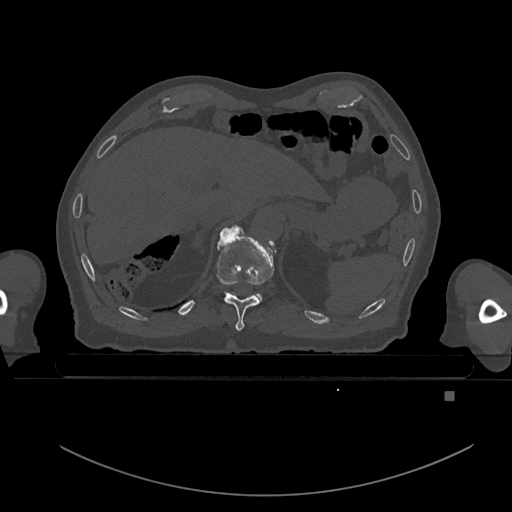
CT including the spine, one axial slice. Slice 76 of 969 in the series (ordered by position). Bone window (W 1800 / L 400 HU). 512 × 512 image matrix, field of view 456 × 456 mm. Male patient, age 82 years. From the clinical record (not read from this slice): primary cancer: prostate.
Annotated regions visible in this slice (semi-automatic segmentation, software-assisted and operator-edited):
- T10 vertebra: bounding box [x1, y1, x2, y2] px = [216, 225, 275, 331]
- T11 vertebra: [254, 294, 262, 301]